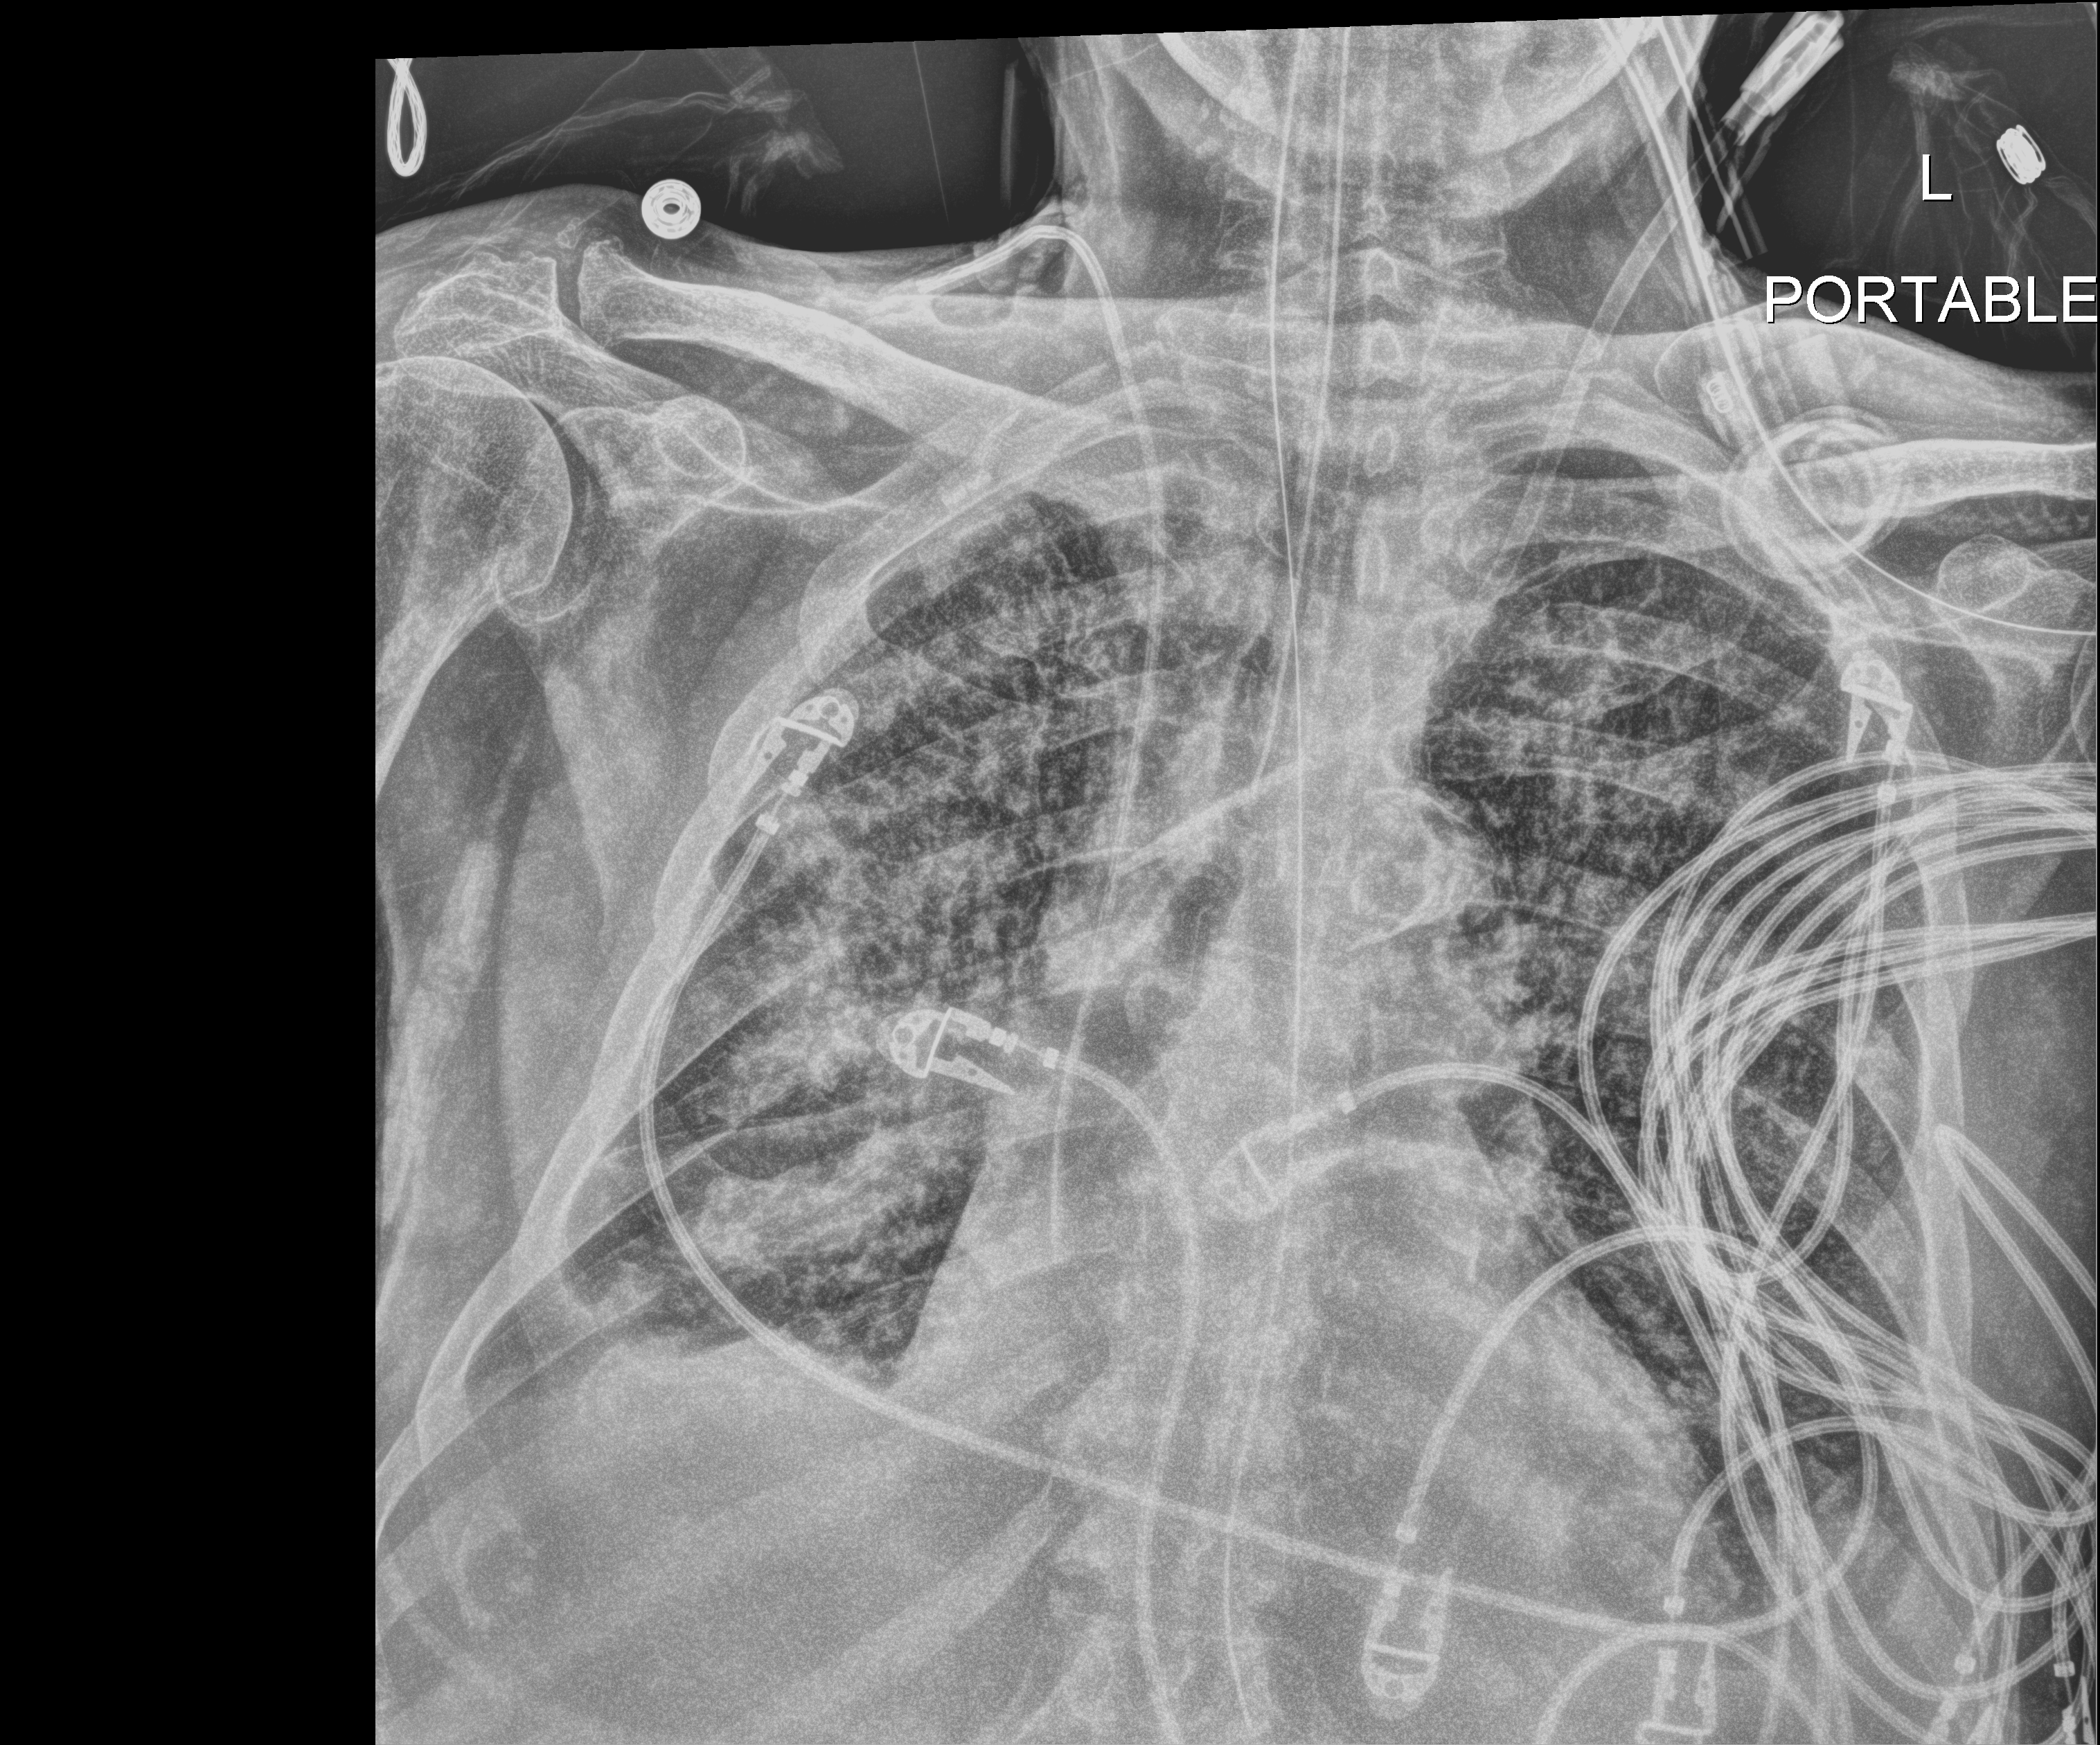
Chest X-ray (portable), anteroposterior (AP) projection. Male patient hospitalised with COVID-19, age 75–90 years.
From the hospital-stay record, not from the radiograph (when in the stay this image was taken is not recorded):
- chronic kidney disease (admission record): no
- admitted to intensive care during this hospital stay: yes